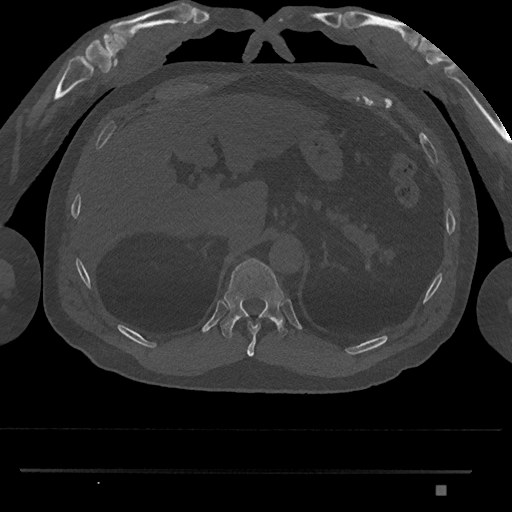
CT including the spine, one axial slice; position 965 of 1134 along the scan axis; reconstruction kernel Br40s/3; 120 kVp; bone window (W 1800 / L 400 HU); 512 × 512 image matrix. Patient: male, 65 years. From the clinical record (not read from this slice): primary cancer: prostate.
Annotated regions visible in this slice (semi-automatically segmented with operator editing):
- T10 vertebra: box from (x=247, y=321) to (x=261, y=357) px
- T11 vertebra: (x=220, y=258)–(x=288, y=339)